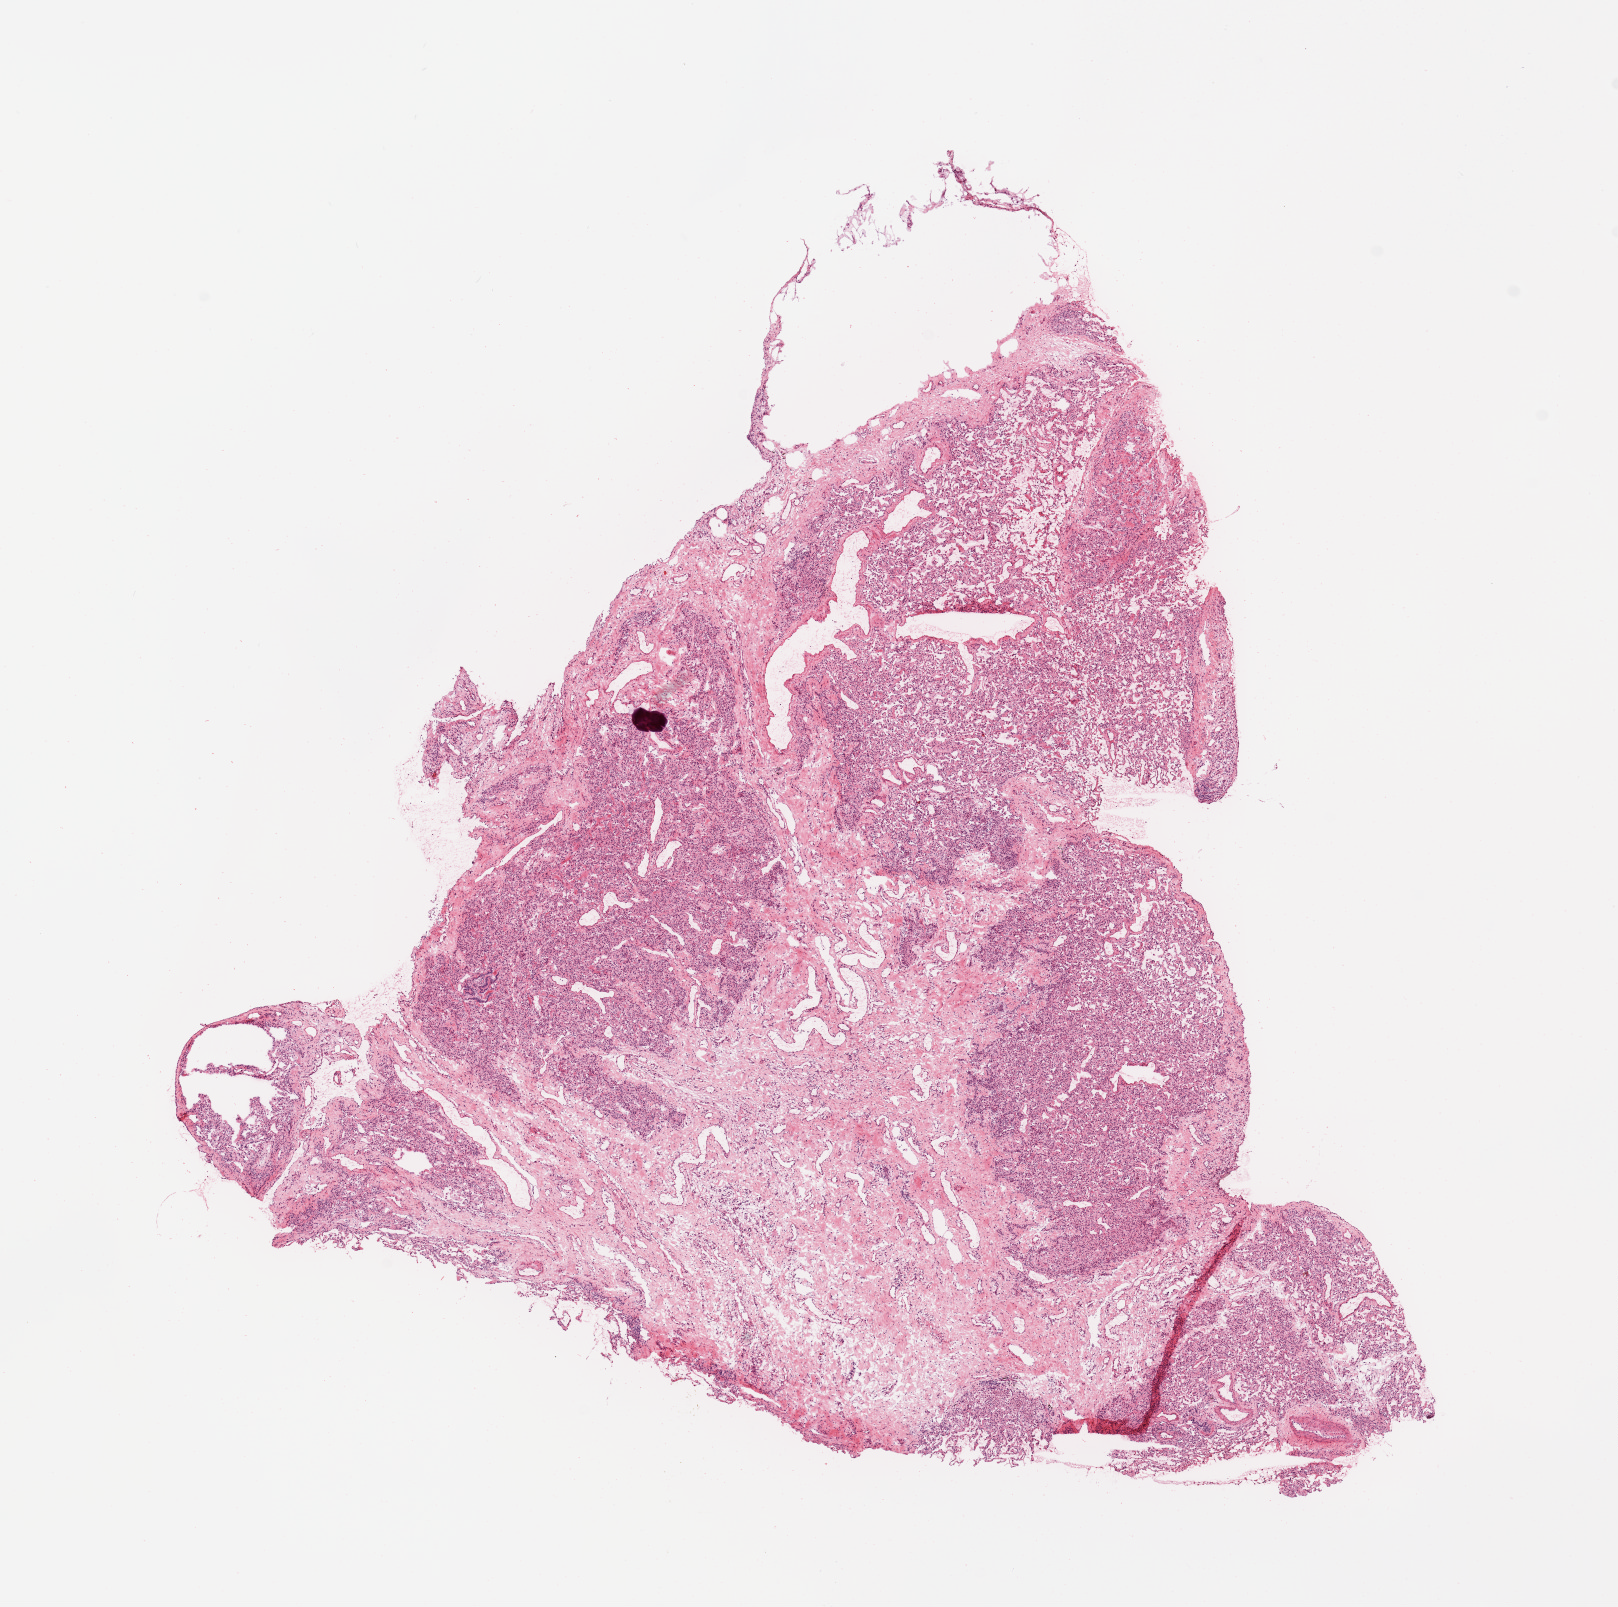
Digitized H&E-stained tissue section (whole slide) — a low-resolution overview of the entire scanned area, about 12.8 x 12.7 mm (acquisition: 20x scan); lung, normal (non-tumour) tissue. Female, 35 y/o.
- this section: normal (non-tumour) tissue from the same patient
- patient diagnosis: Adenocarcinoma, NOS